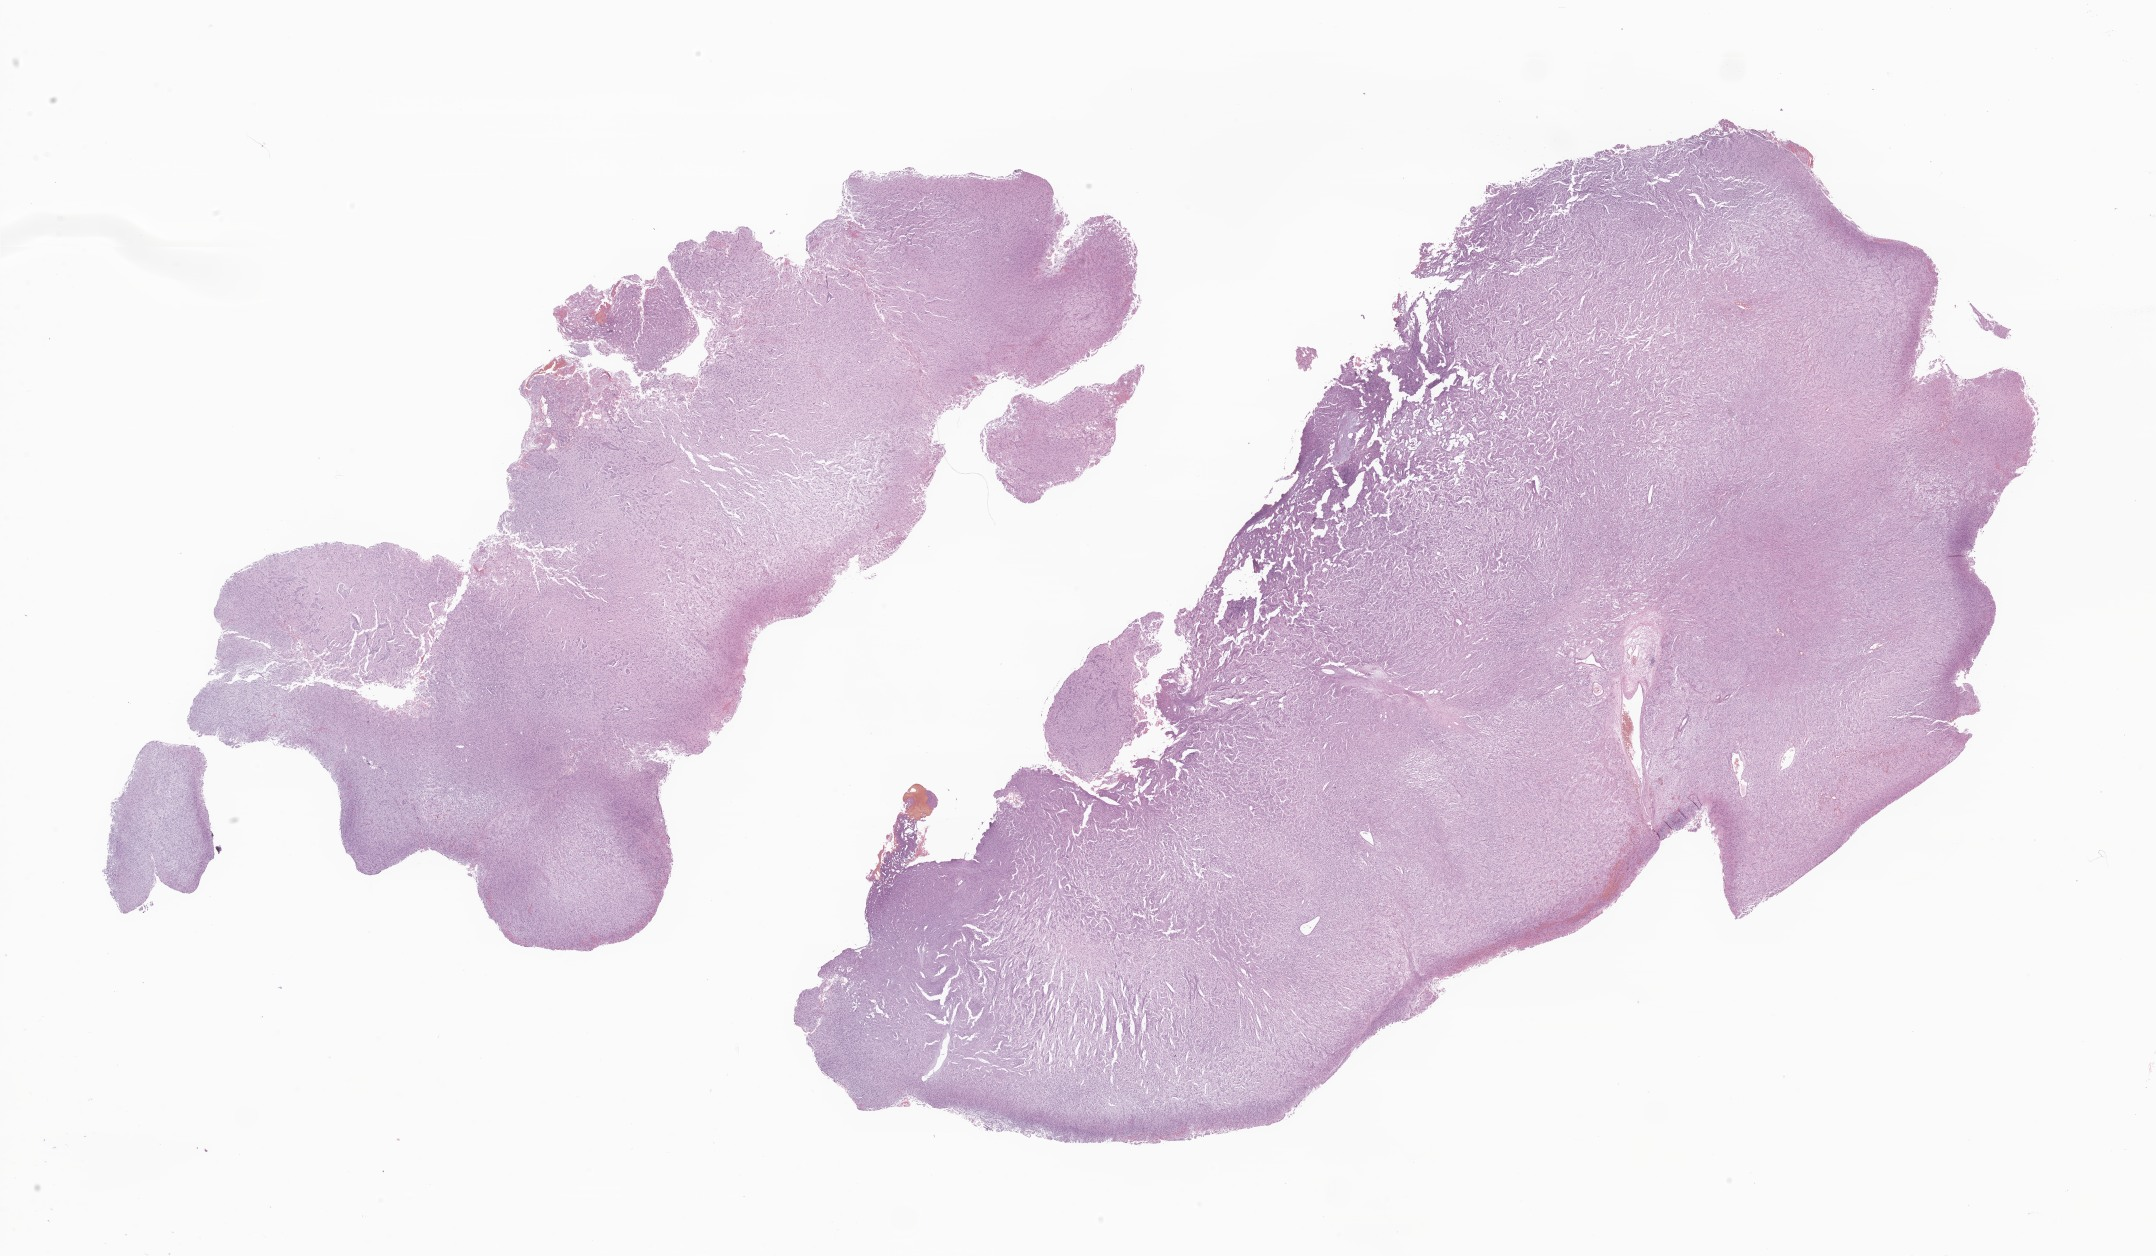
Digitized H&E-stained section of tumor tissue from the brain, shown as a low-resolution overview of the whole scanned area (about 36.4 x 21.2 mm), formalin-fixed, paraffin-embedded (FFPE) tissue. Patient female; age 949 days (about 2.6 years).
• diagnosis (ICD-O-3 morphology term): Neoplasm, uncertain whether benign or malignant